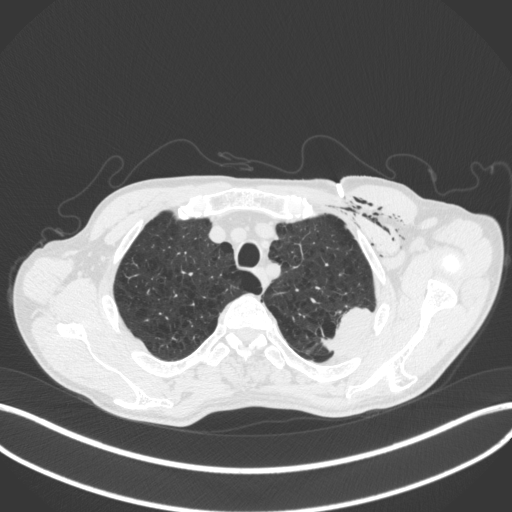
Chest CT, one axial slice; slice 347 of 416 in the series (ordered by position); 120 kVp; lung window (W 1500 / L -600 HU); 1 mm slice thickness; 512 × 512 image matrix, field of view 400 × 400 mm. Patient: male, 58 years. From the clinical record (not read from this slice): clinical TNM (as recorded): T3 N0 M0.
Structures marked on this image (rectangle marked by the reading radiologist):
- lung tumour (recorded histology: adenocarcinoma): bounding box <320,306,376,357> (left, top, right, bottom; pixels)